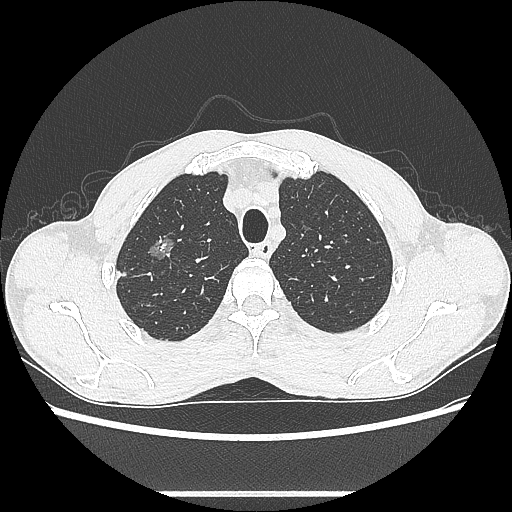
Chest CT, one axial slice. Slice 491 of 601 in the series (ordered by position). Lung window (W 1500 / L -600 HU). 0.62 mm slice thickness. 512 × 512 image matrix, field of view 357 × 357 mm. Male patient, age 54 years. From the clinical record (not read from this slice): clinical TNM (as recorded): T1a N0 M0.
Annotated regions visible in this slice (bounding box drawn by a radiologist):
- lung tumour (recorded histology: adenocarcinoma): bounding box [x1, y1, x2, y2] px = [141, 231, 185, 269]